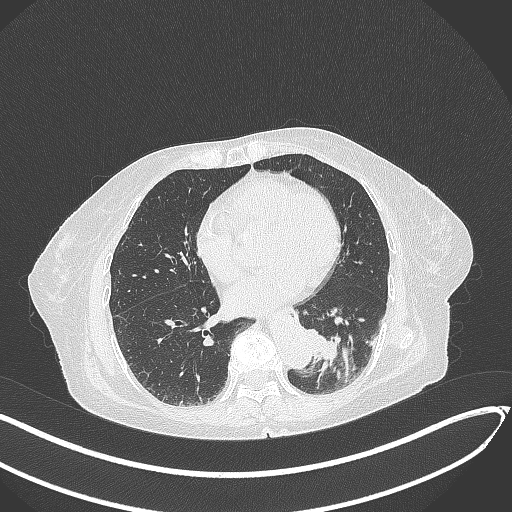
Chest CT, one axial slice. Position 93 of 324 along the scan axis. Reconstruction kernel B70f. 120 kVp. Lung window (W 1500 / L -600 HU). 512 × 512 image matrix, field of view 400 × 400 mm. Female patient, age 82 years. From the clinical record (not read from this slice): clinical TNM (as recorded): T1b N0 M1.
Annotated regions visible in this slice (rectangle marked by the reading radiologist):
- lung tumour (recorded histology: adenocarcinoma): box from (x=299, y=323) to (x=346, y=370) px